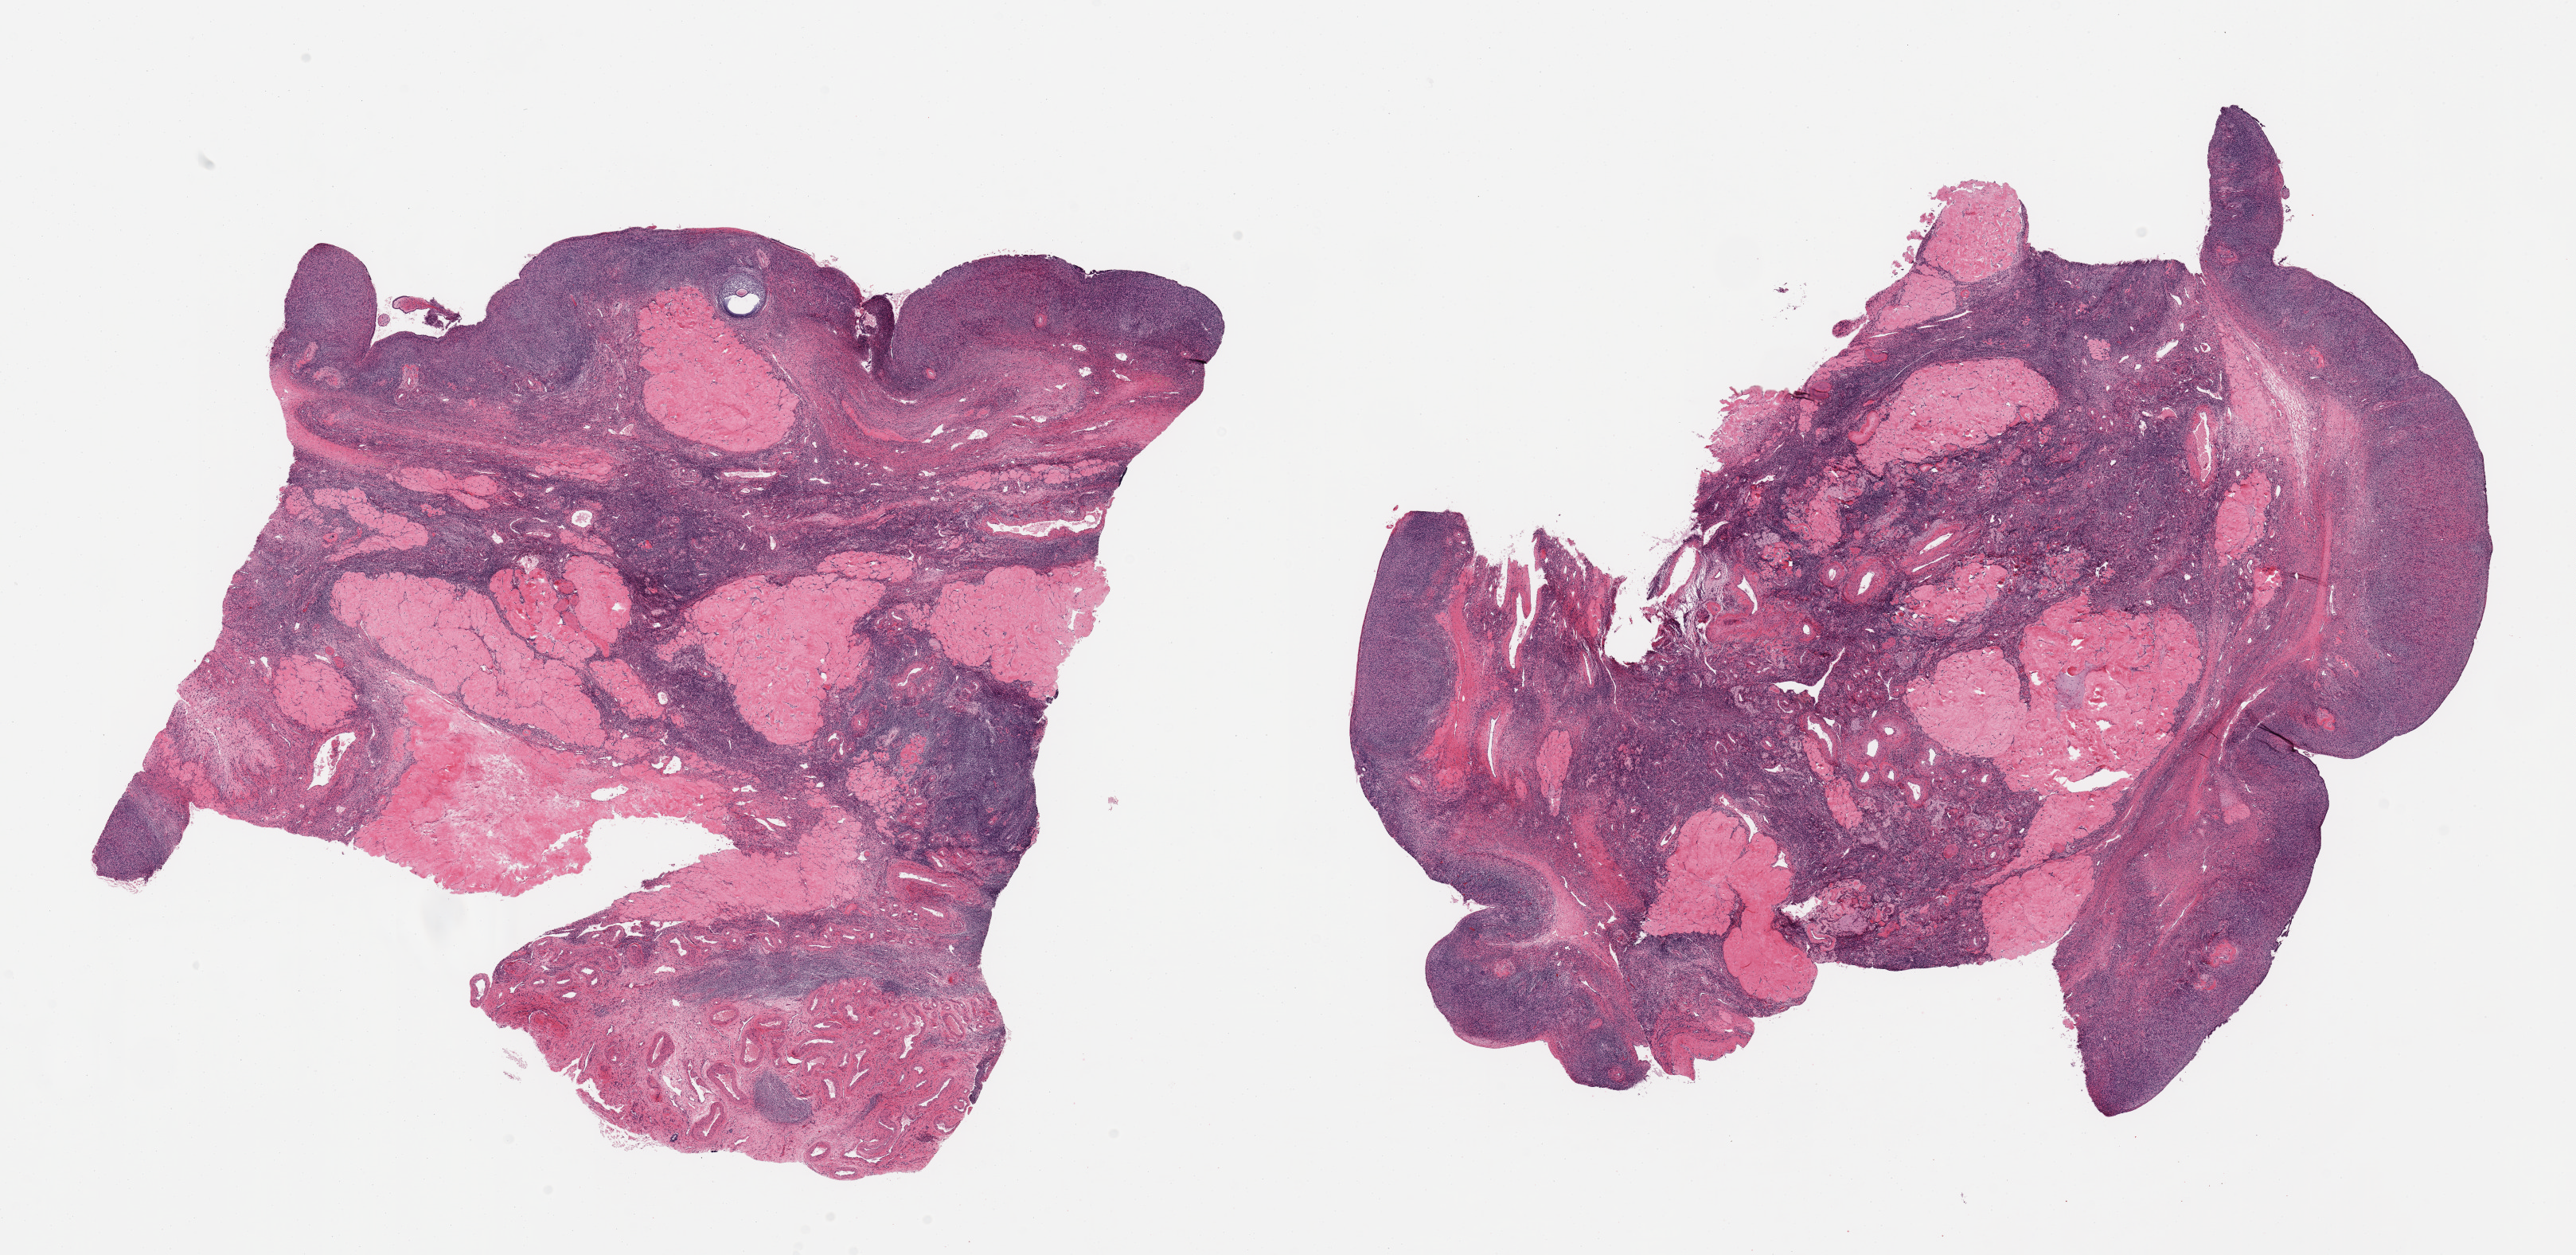
H&E whole-slide image, low-resolution overview of the scanned area, about 25.6 x 12.5 mm (acquisition: 20x scan); PAXgene-fixed paraffin-embedded (PFPE) section; section of ovary (target tissue); donor tissue sample. Donor: female.
Pathologist's review note for this sample: 2 pieces, post menopausal involutional changes.